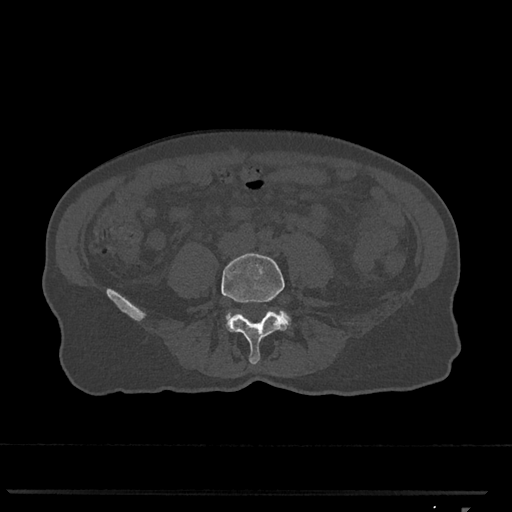
CT including the spine, one axial slice; slice 196 of 793 in the series (ordered by position); reconstruction kernel Br40s/3; 120 kVp; bone window (W 1800 / L 400 HU); 512 × 512 image matrix. Patient: female, 62 years. From the clinical record (not read from this slice): primary cancer: renal.
Outlined on this slice (semi-automatically segmented with operator editing):
- L4 vertebra: bounding box <221,253,286,365> (left, top, right, bottom; pixels)
- L5 vertebra: <226,311,291,329>